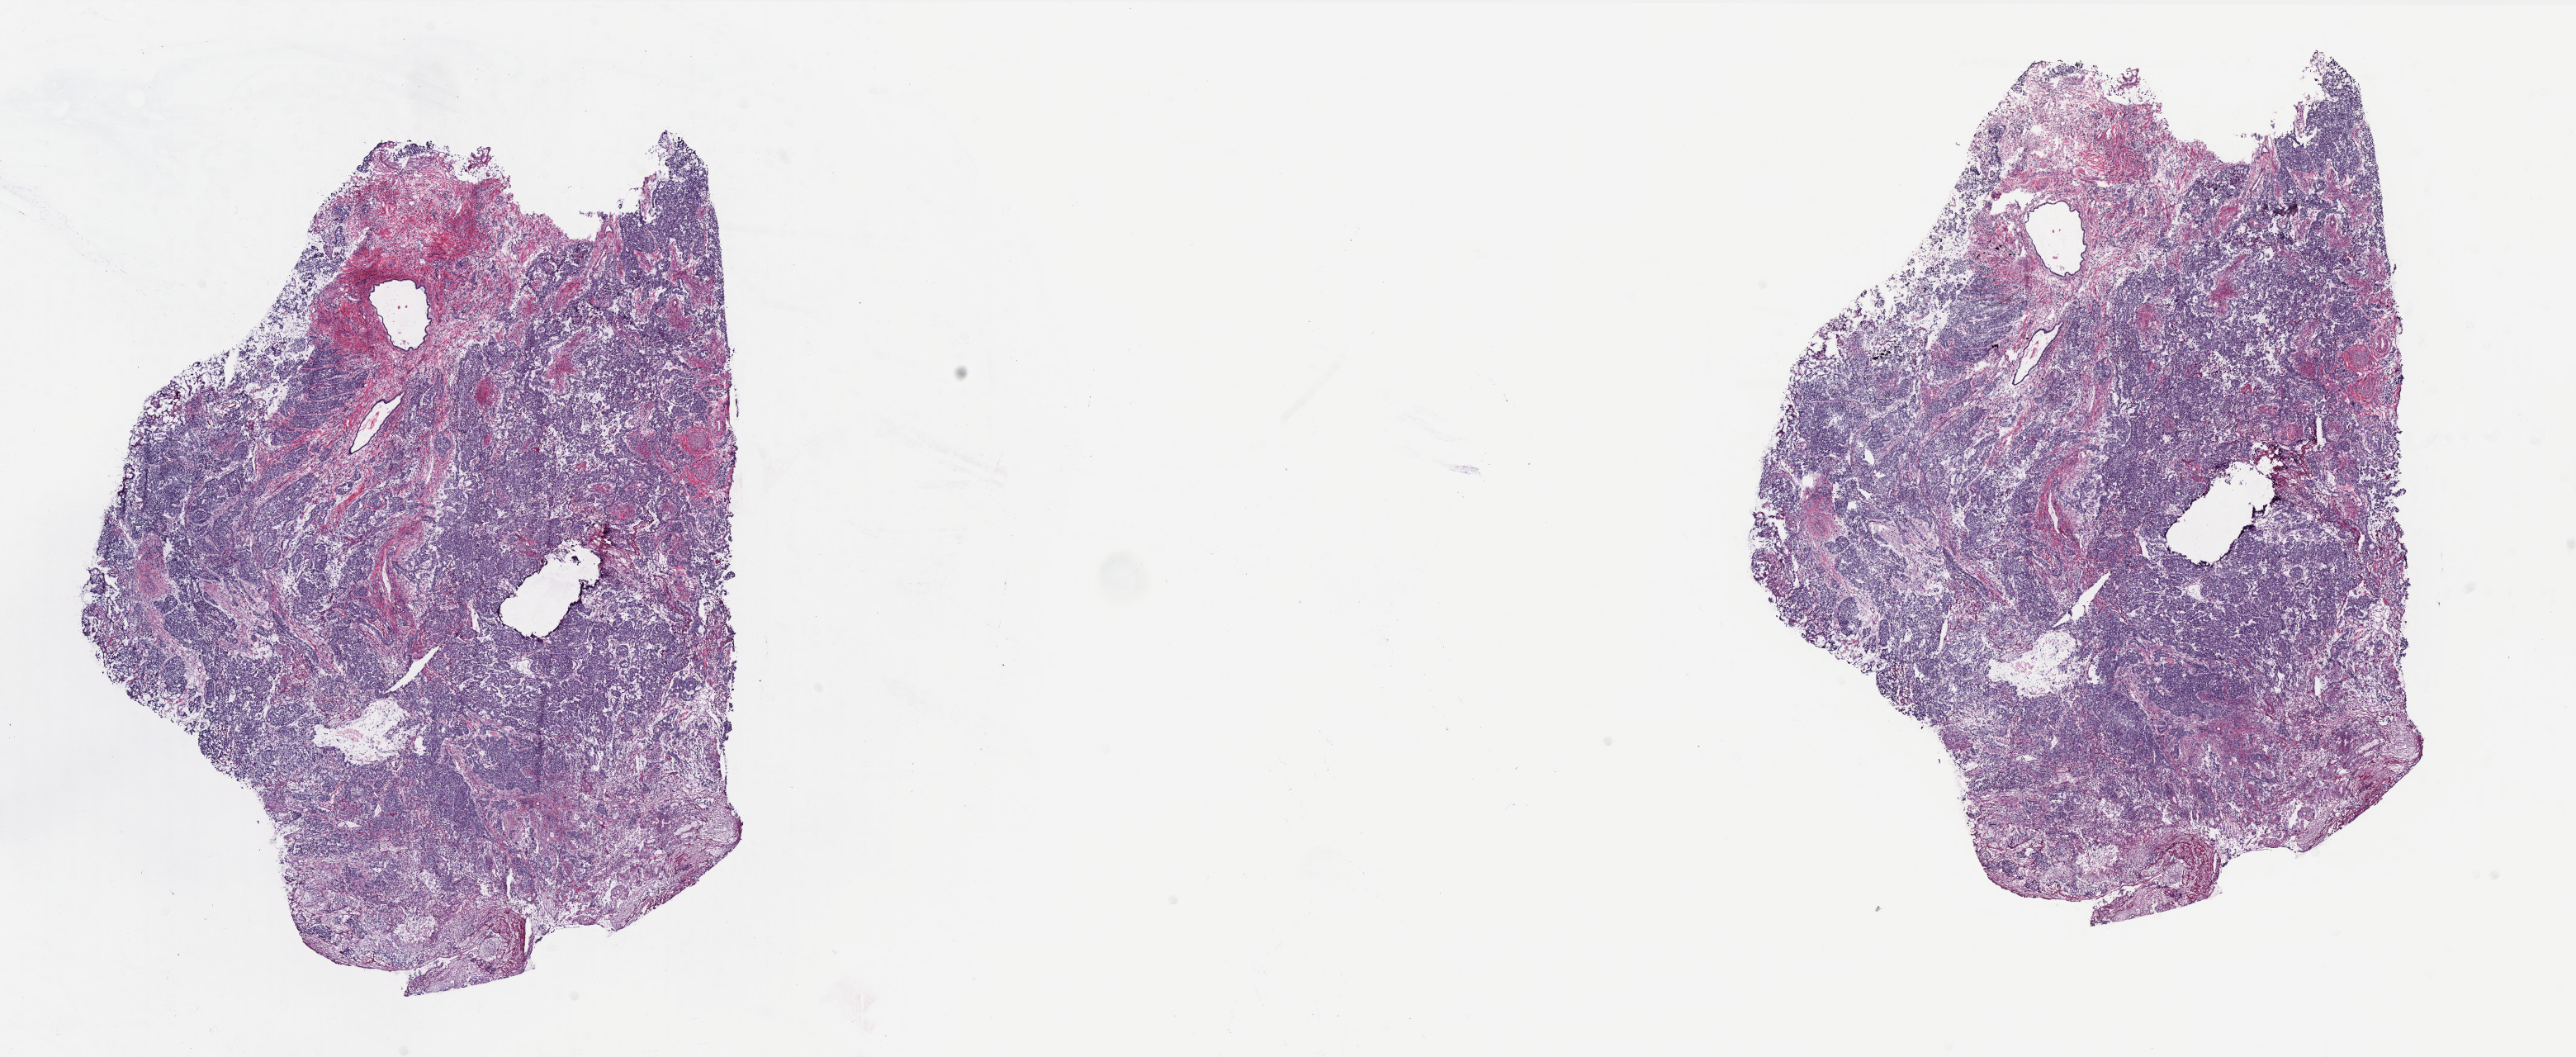
Whole-slide histology image, H&E-stained — low-resolution overview of the scanned area, about 25.0 x 10.3 mm (from a 40x scan). Frozen section. Uterus, primary tumour sample. Female patient; age at initial diagnosis 69 years. Histologic grade: G3 (poorly differentiated). Composition of this section per pathologist review: tumour cells 70%, tumour nuclei 70%, normal cells 0%, stromal cells 30%, necrosis 0%. Infiltration values recorded for this section: lymphocyte infiltration 0%, monocyte infiltration 0%, neutrophil infiltration 0%.
Histologic diagnosis: Serous cystadenocarcinoma, NOS. FIGO stage: IIIC.